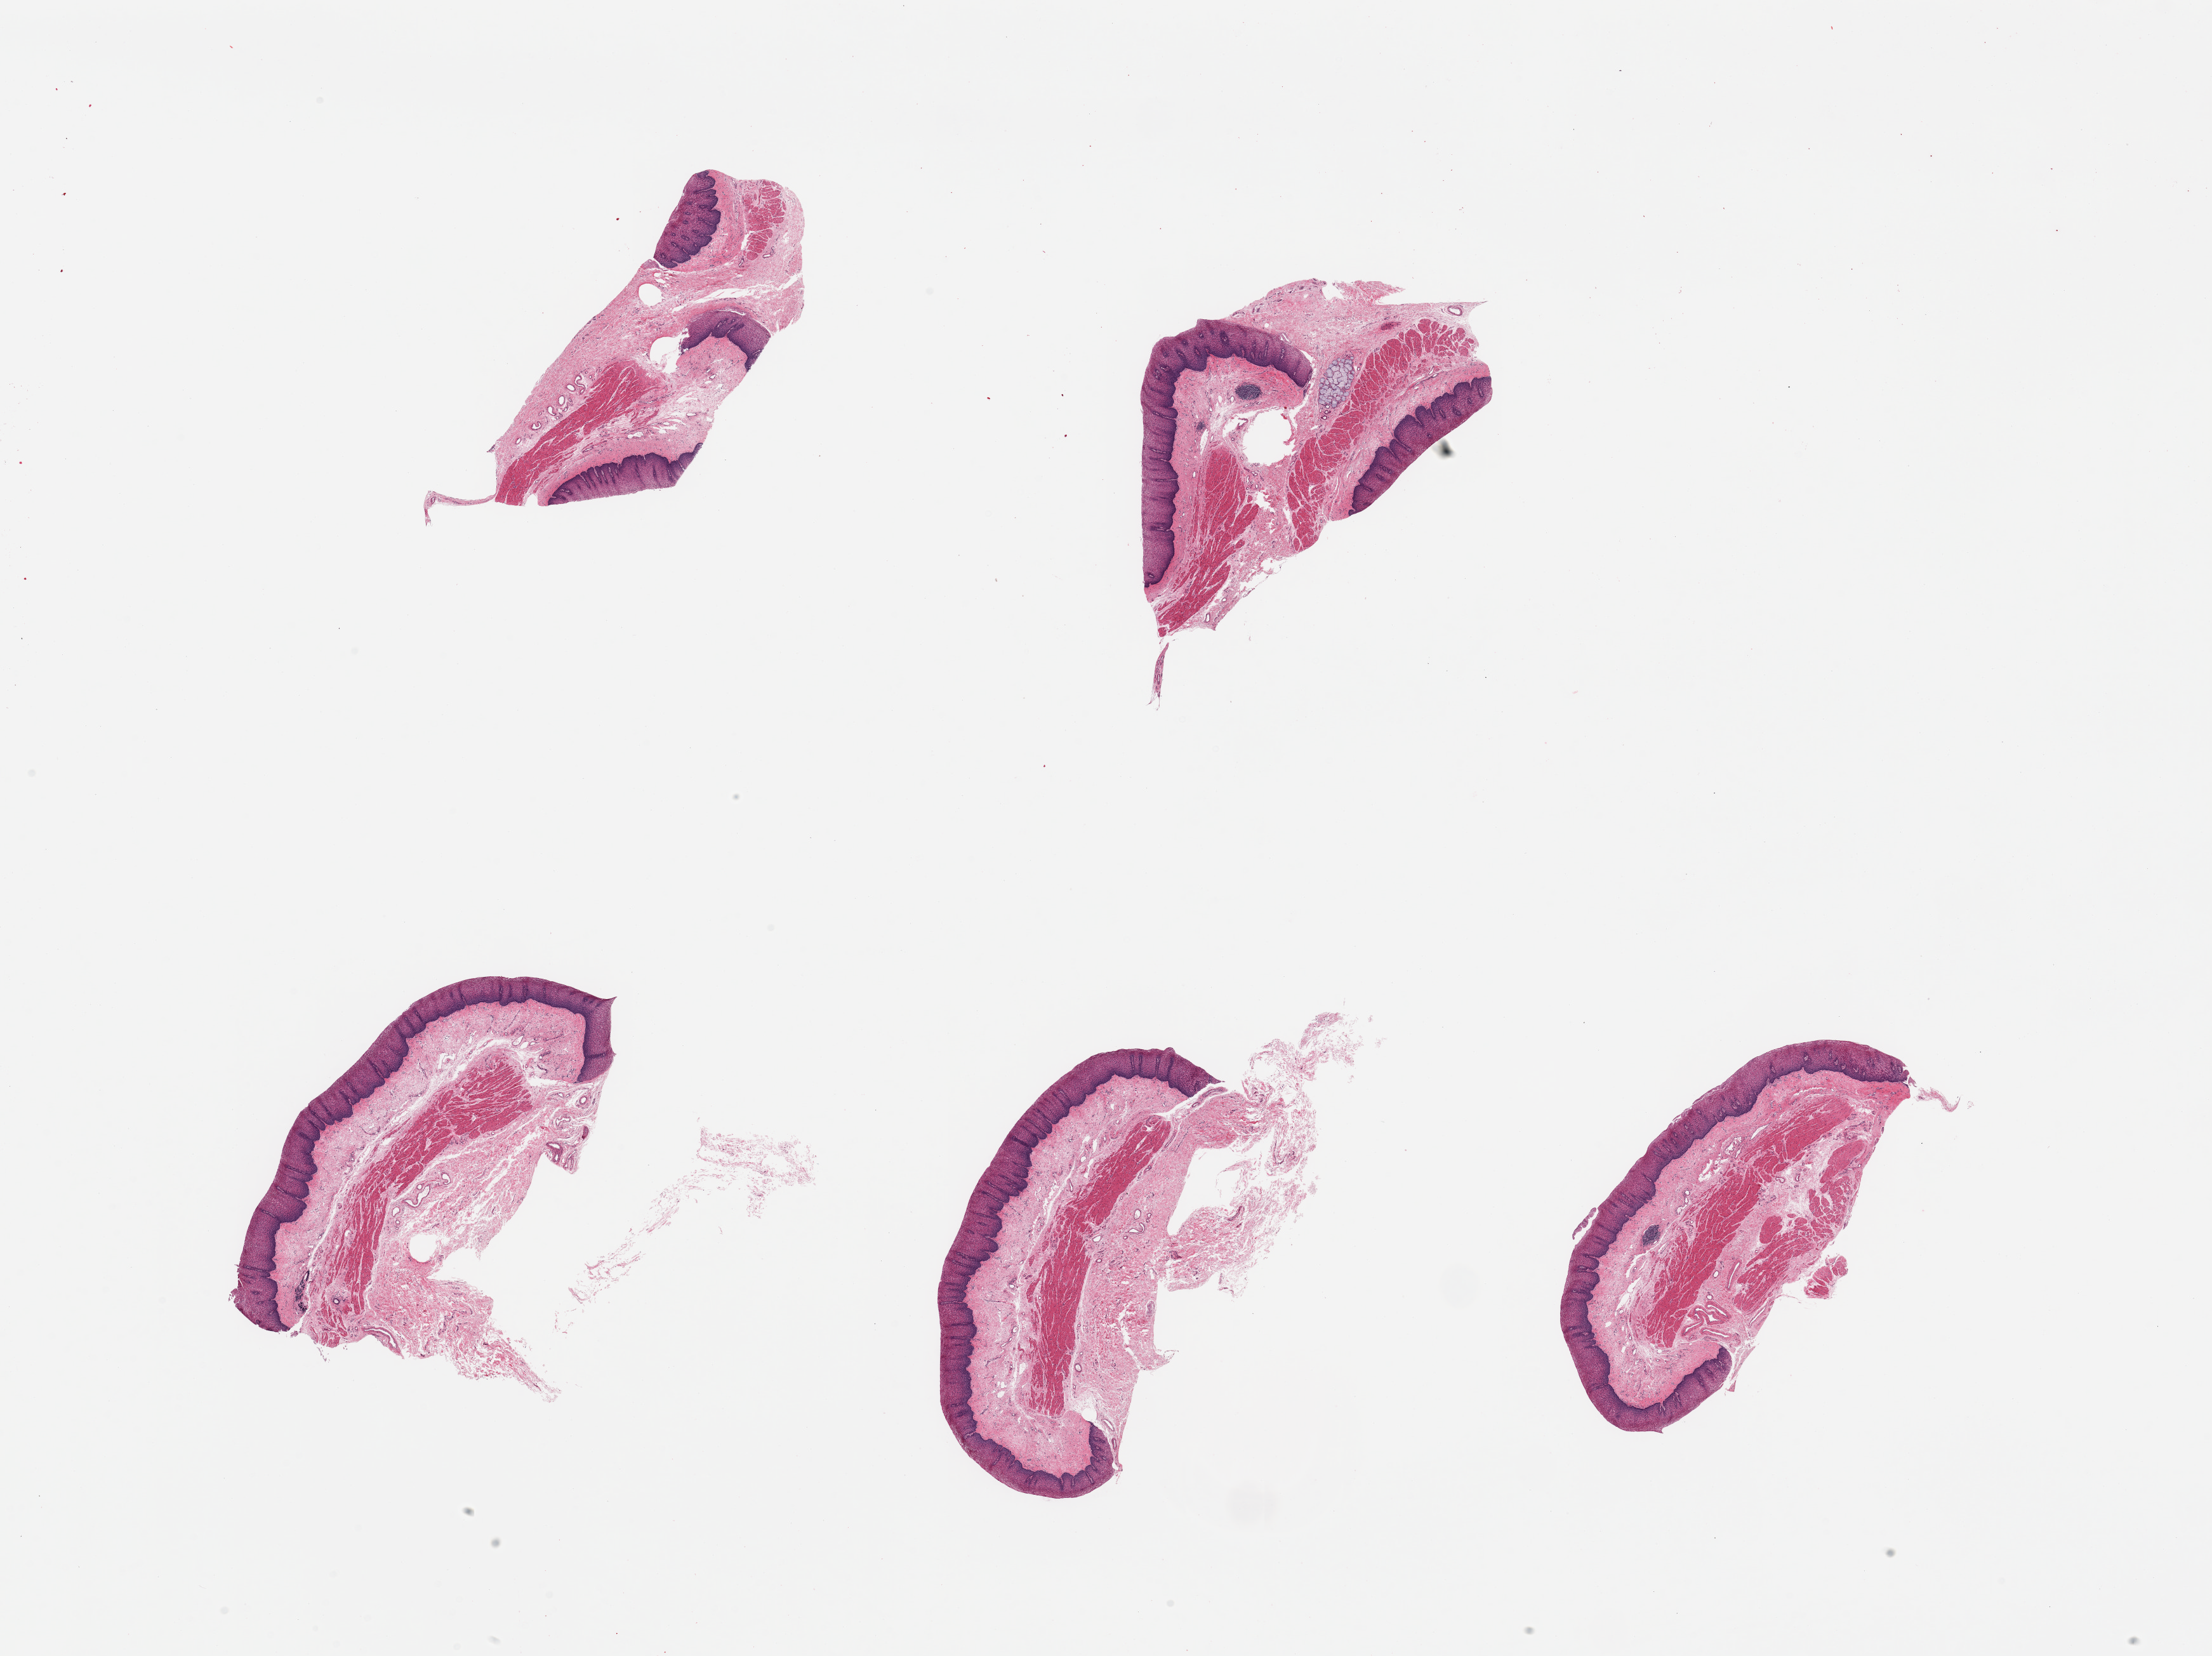
Digitized haematoxylin and eosin-stained section, brightfield — low-resolution overview of the scanned area, about 27.6 x 20.6 mm. PAXgene-fixed, paraffin-embedded tissue. Sampled site (target tissue): esophageal mucous membrane. Donor tissue sample. Donor sex: female.
Review note (as recorded): 6 pieces, squamous mucosa is ~0.4mm, 15-20% thickness.